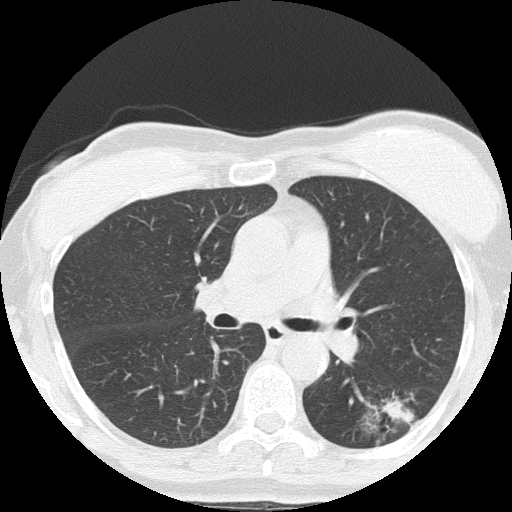
Low-dose screening chest CT, one axial slice; reconstruction kernel FC51; 120 kVp; lung window (W 1500 / L -600 HU); 2 mm slice thickness; 512 × 512 image matrix, field of view 308 × 308 mm.
Annotated regions visible in this slice (outlined manually by an expert reader):
- lesion 1 (tumor, lower lobe of left lung): bounding box [x1, y1, x2, y2] px = [385, 398, 413, 423]